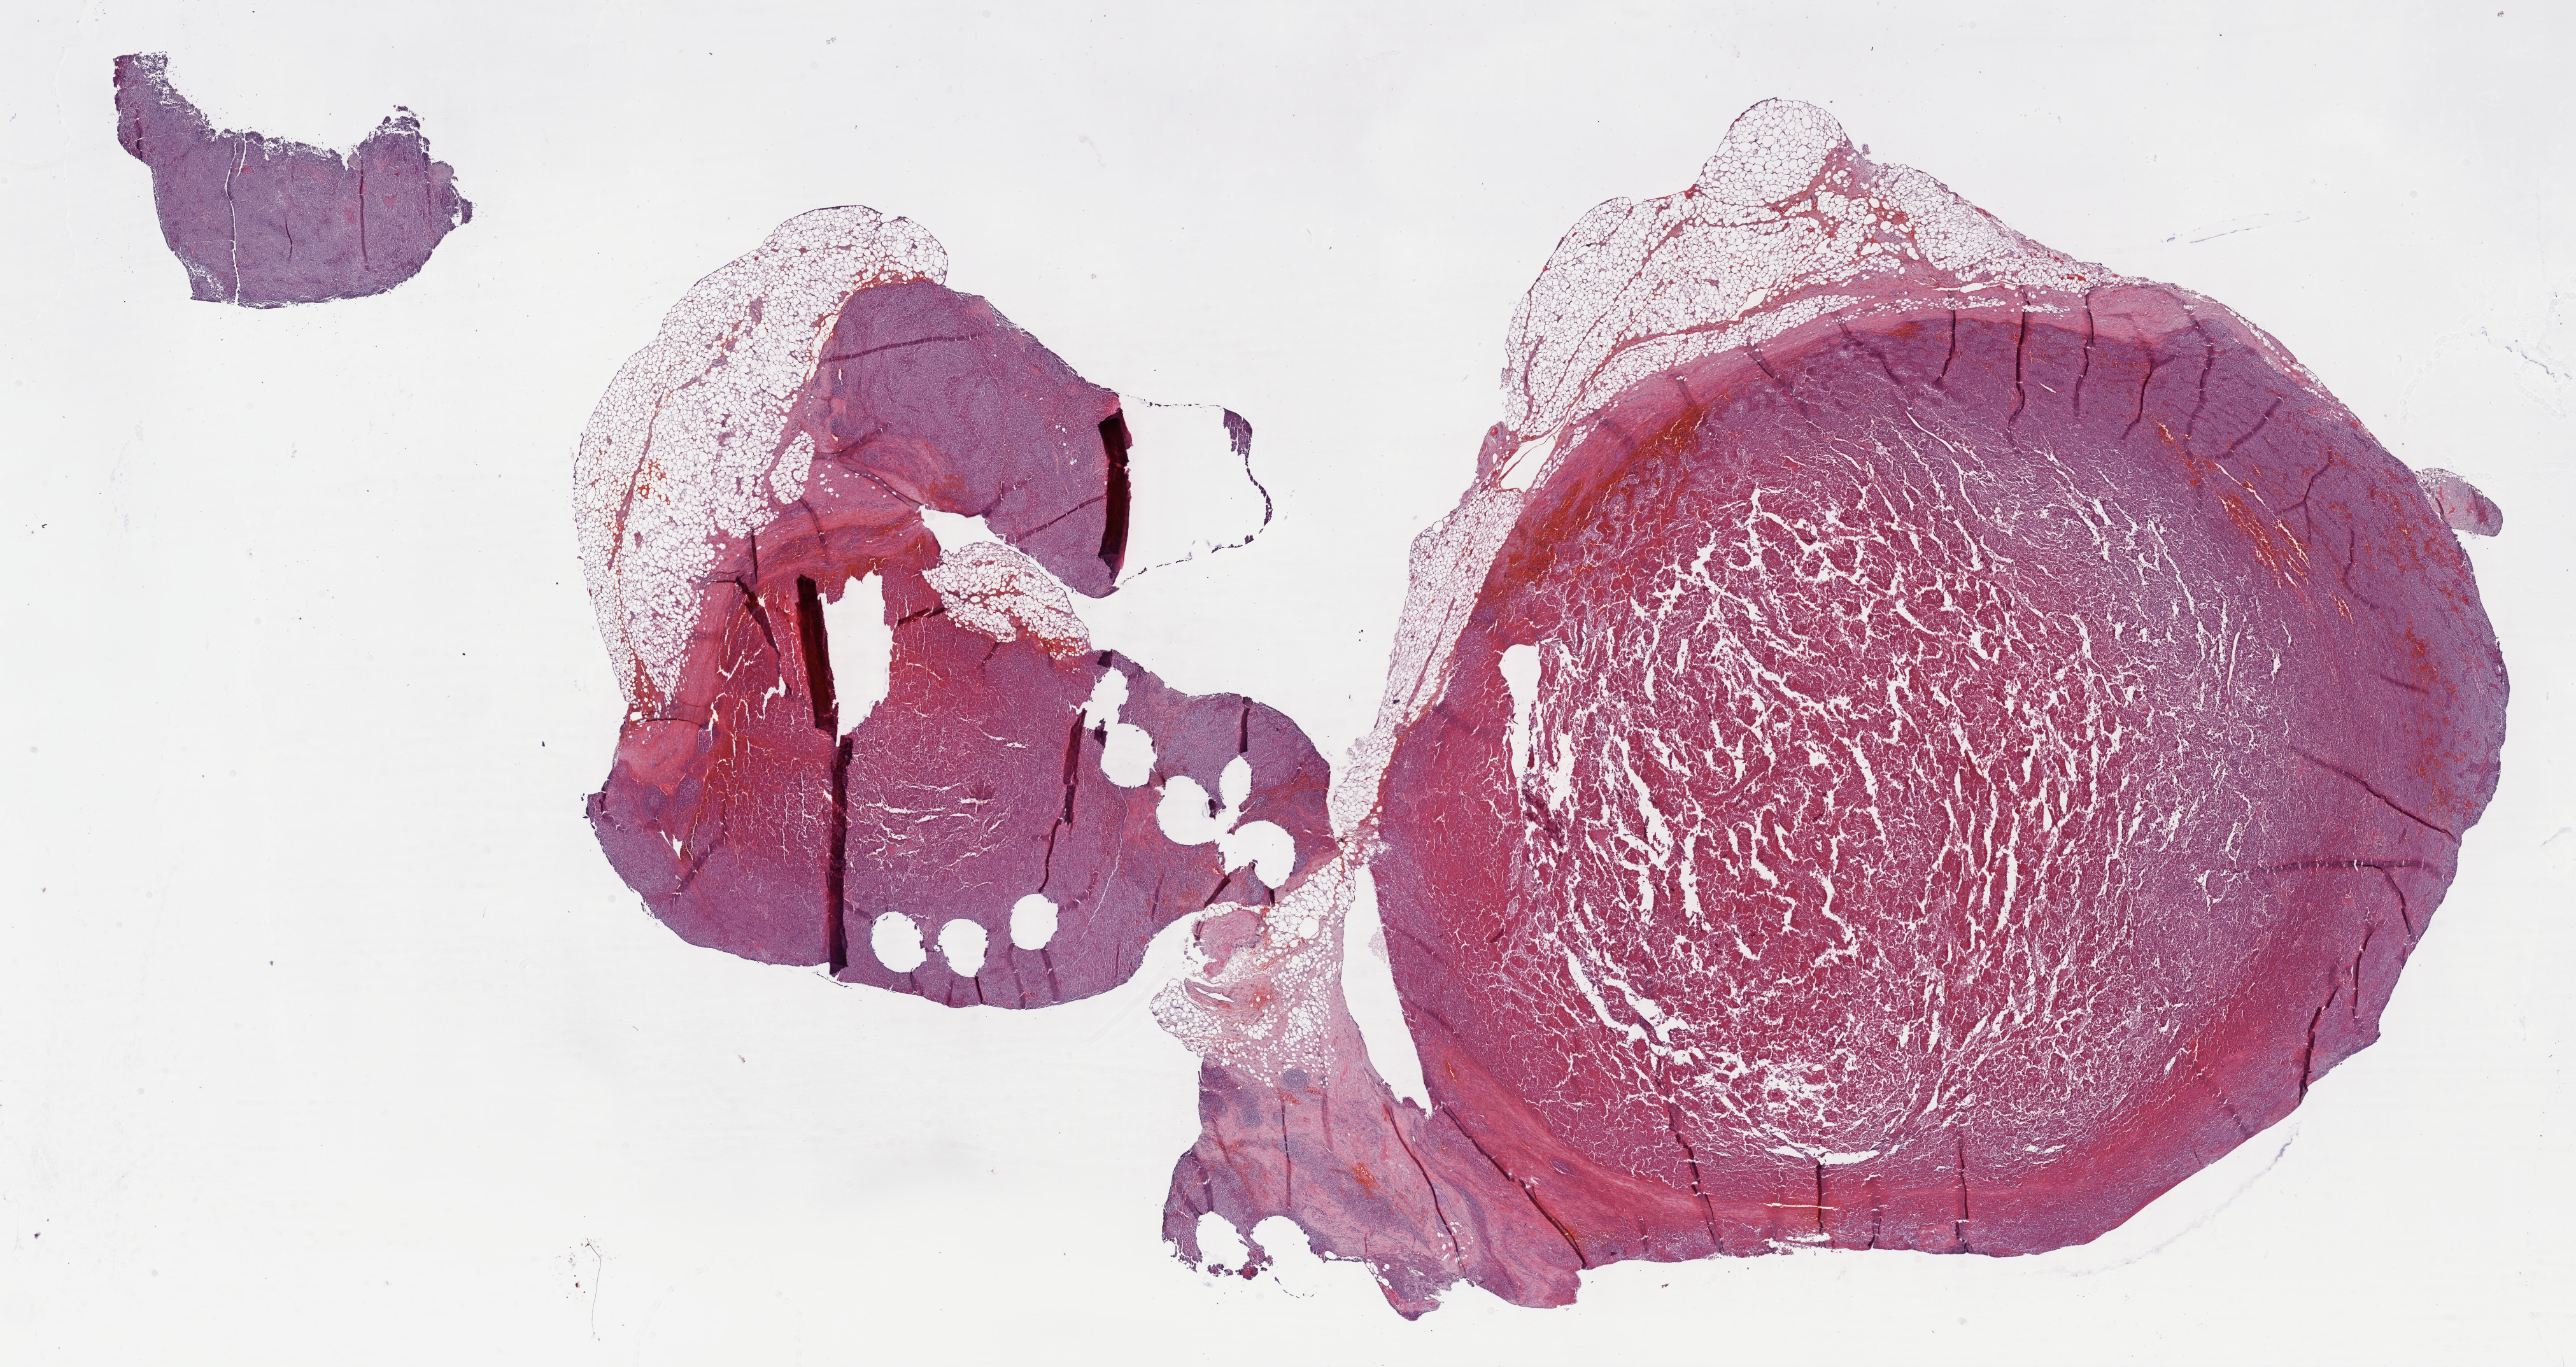
Whole-slide histology image, Hematoxylin and eosin (H&E) stained — a low-resolution overview of the entire scanned area, about 32.7 x 17.4 mm (acquisition: 40x scan), formalin-fixed paraffin-embedded (FFPE) diagnostic section, skin, primary tumour sample. Male patient; age at initial diagnosis 64 years.
Diagnosis: Malignant melanoma, NOS.